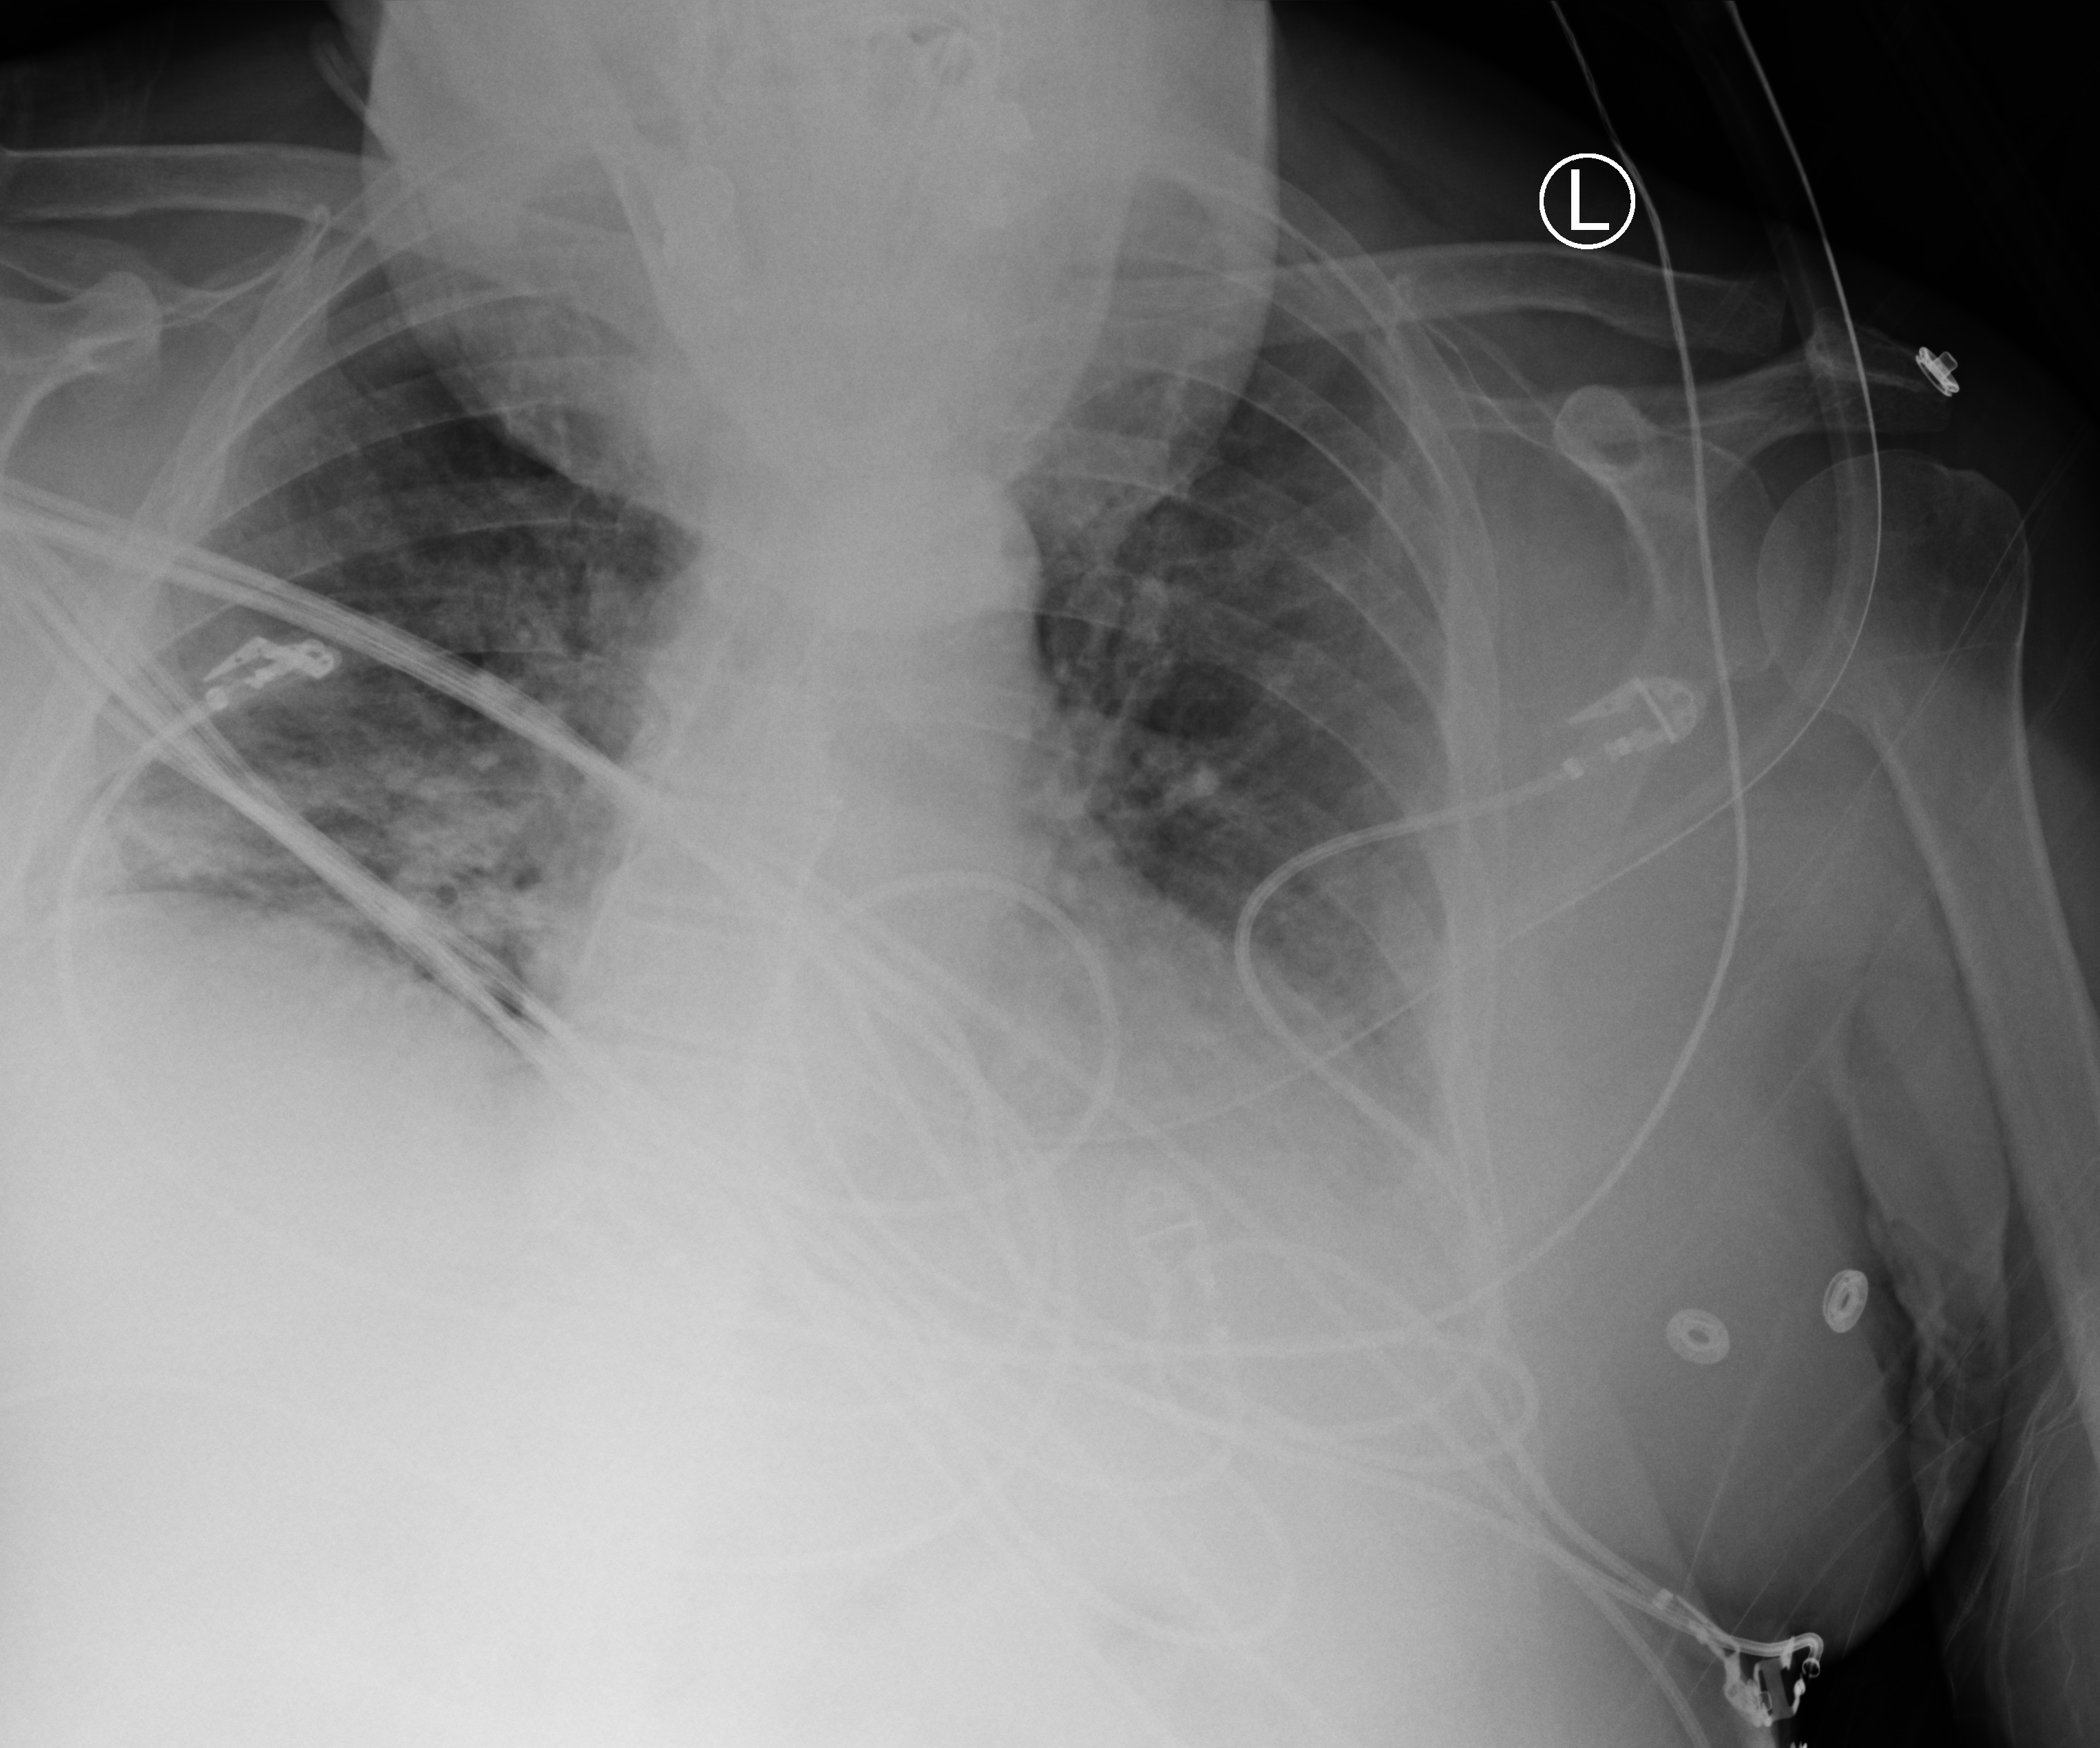
Portable chest radiograph, anteroposterior (AP) projection. Male patient hospitalised with COVID-19, age 60–74 years.
Hospital-stay facts (about this admission, not read from this image; timing relative to this image not recorded):
- mechanically ventilated during this hospital stay: yes
- admitted to intensive care during this hospital stay: yes
- length of hospital stay: 26 days